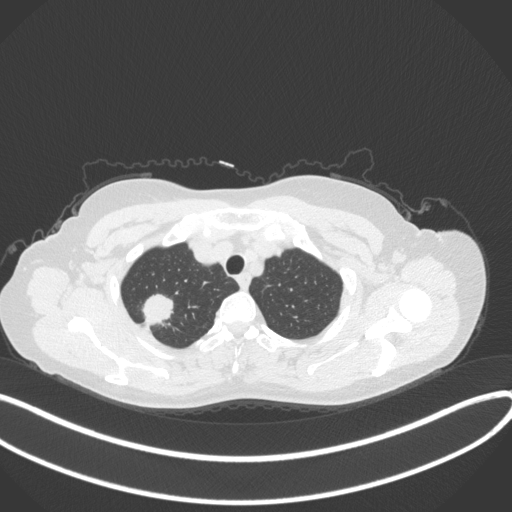
Chest CT, one axial slice. Position 313 of 342 along the scan axis. 120 kVp. Lung window (W 1500 / L -600 HU). 1 mm slice thickness. 512 × 512 image matrix. Patient: female, 50 years. From the clinical record (not read from this slice): clinical TNM (as recorded): T1c N0 M0; histopathological grade: G2-3.
Annotated regions visible in this slice (bounding box drawn by a radiologist):
- lung tumour (recorded histology: adenocarcinoma): bounding box (x1, y1, x2, y2) in pixels: (142, 290, 176, 328)